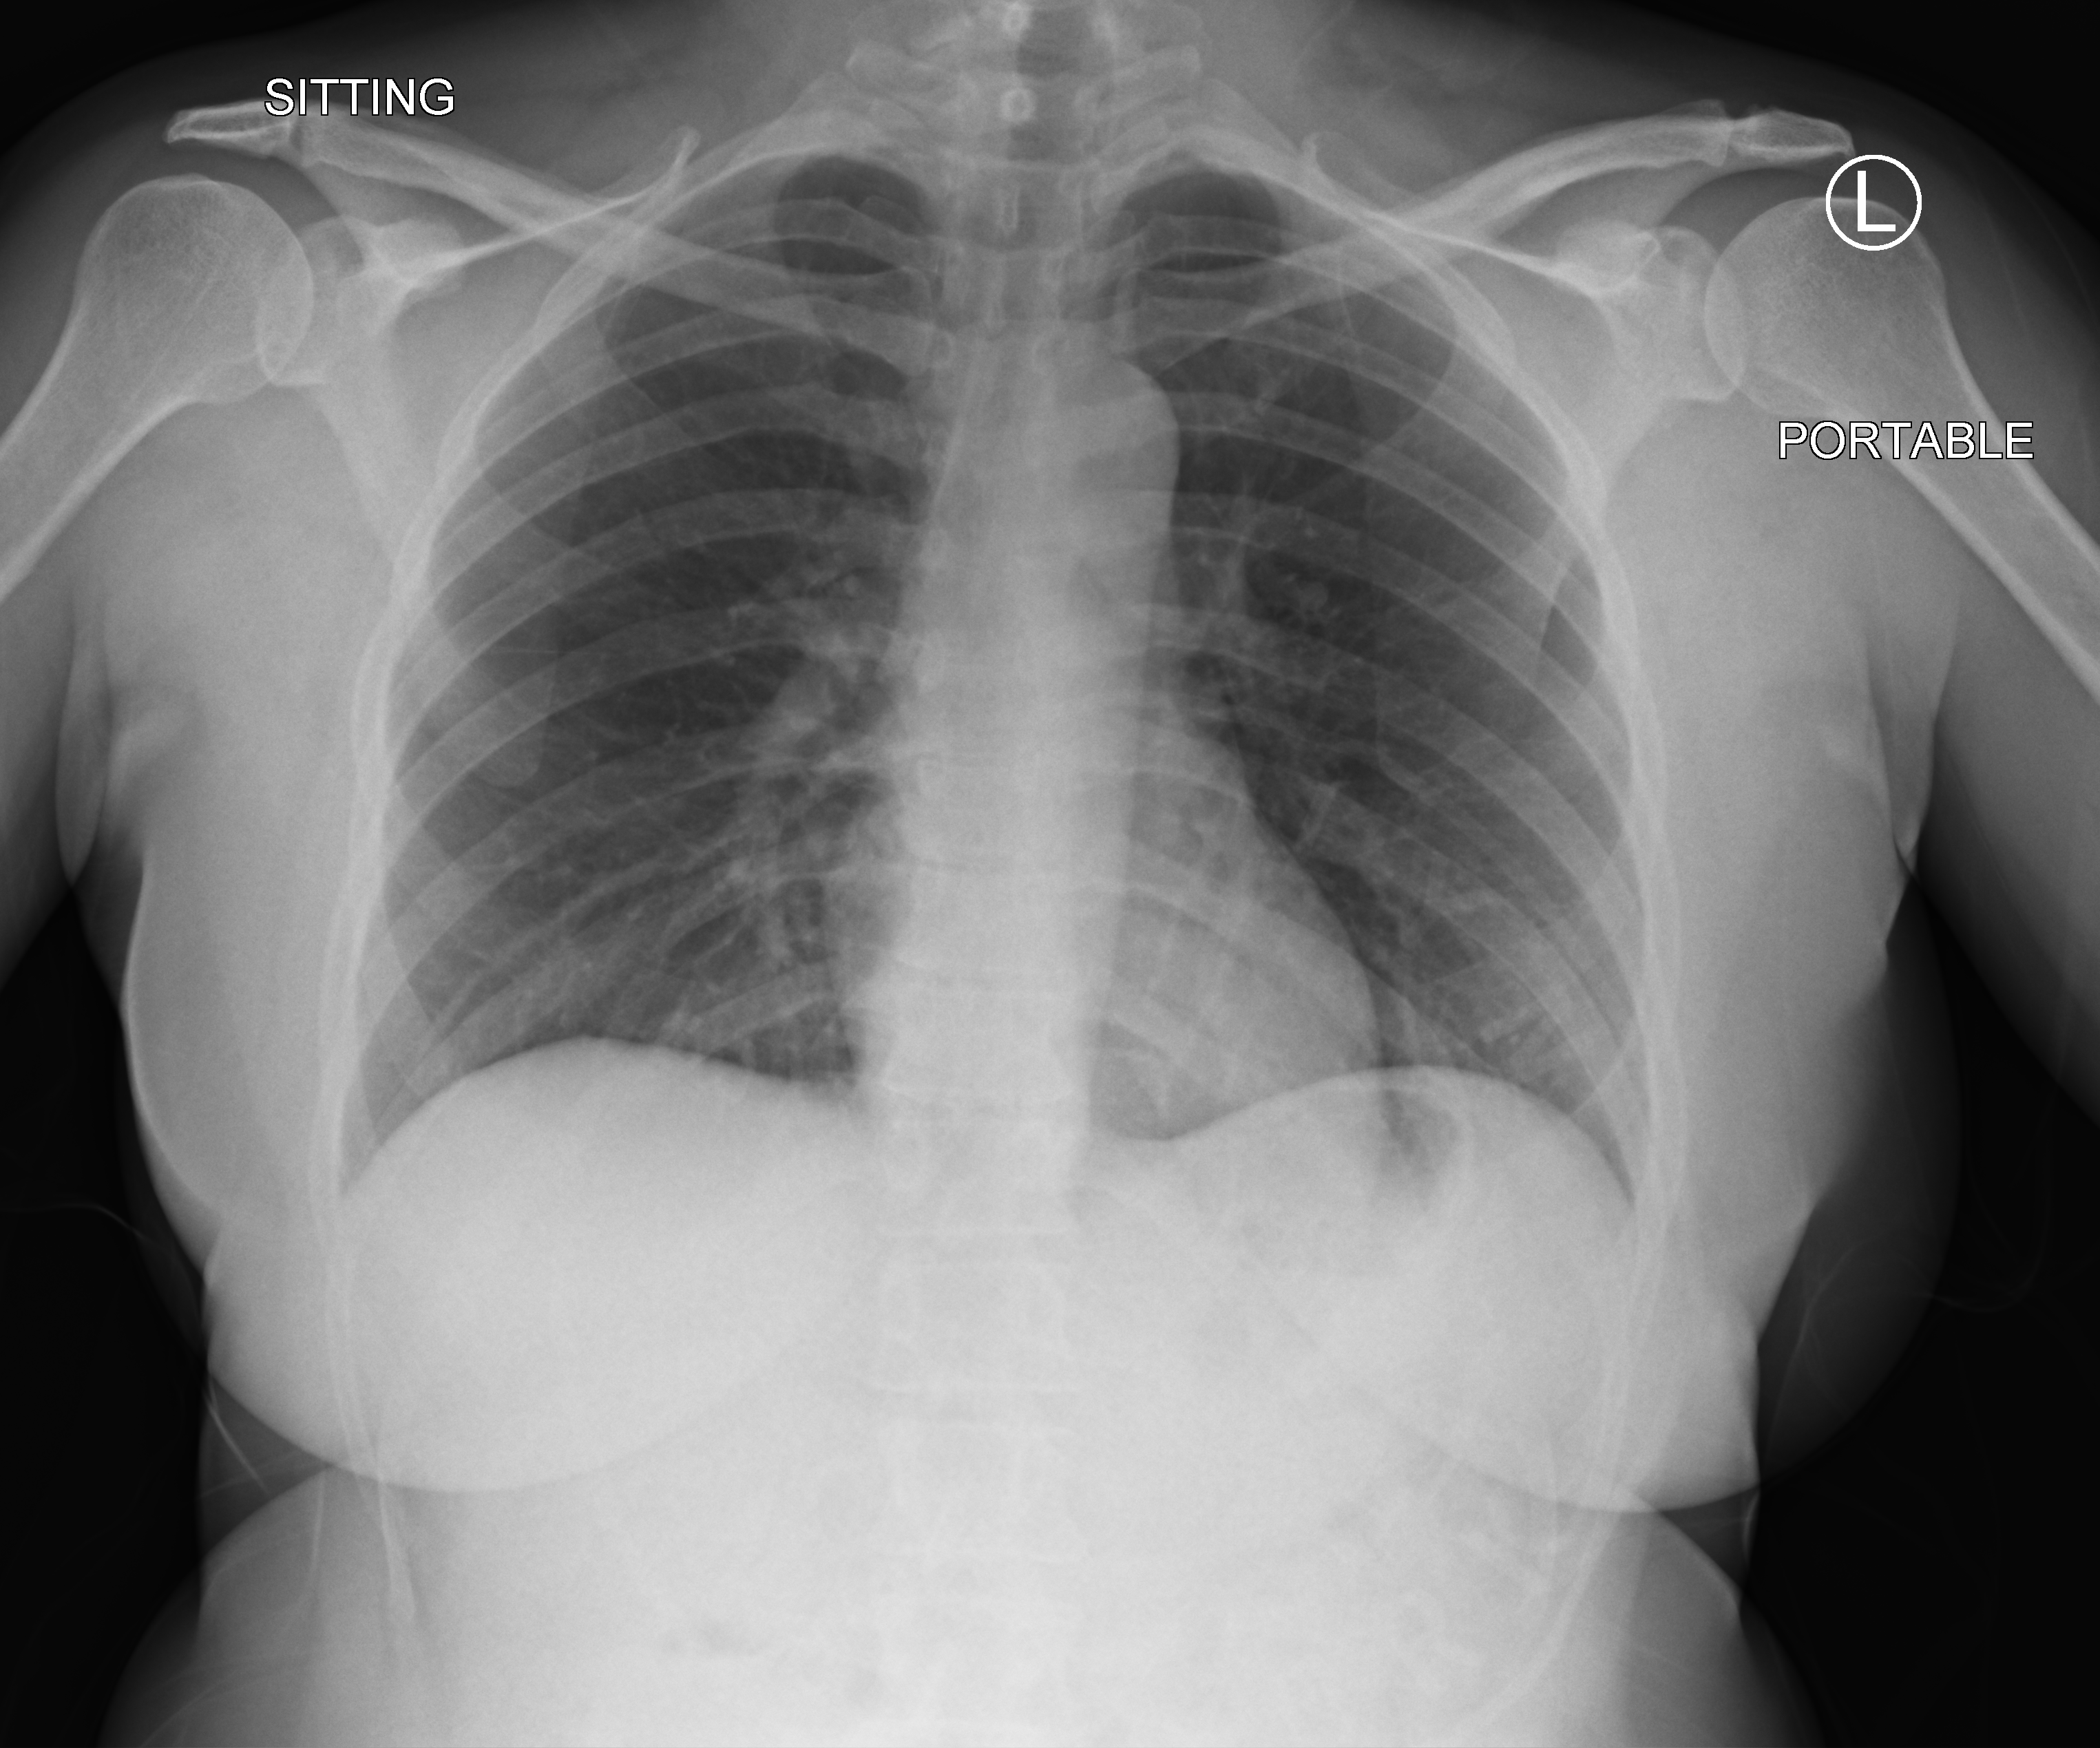
Bedside chest radiograph (computed radiography), anteroposterior (AP) projection. Female patient hospitalised with COVID-19, age 18–59 years.
Admission-level facts for this patient (not findings on this image; timing relative to this image not recorded): mechanically ventilated during this hospital stay: no.